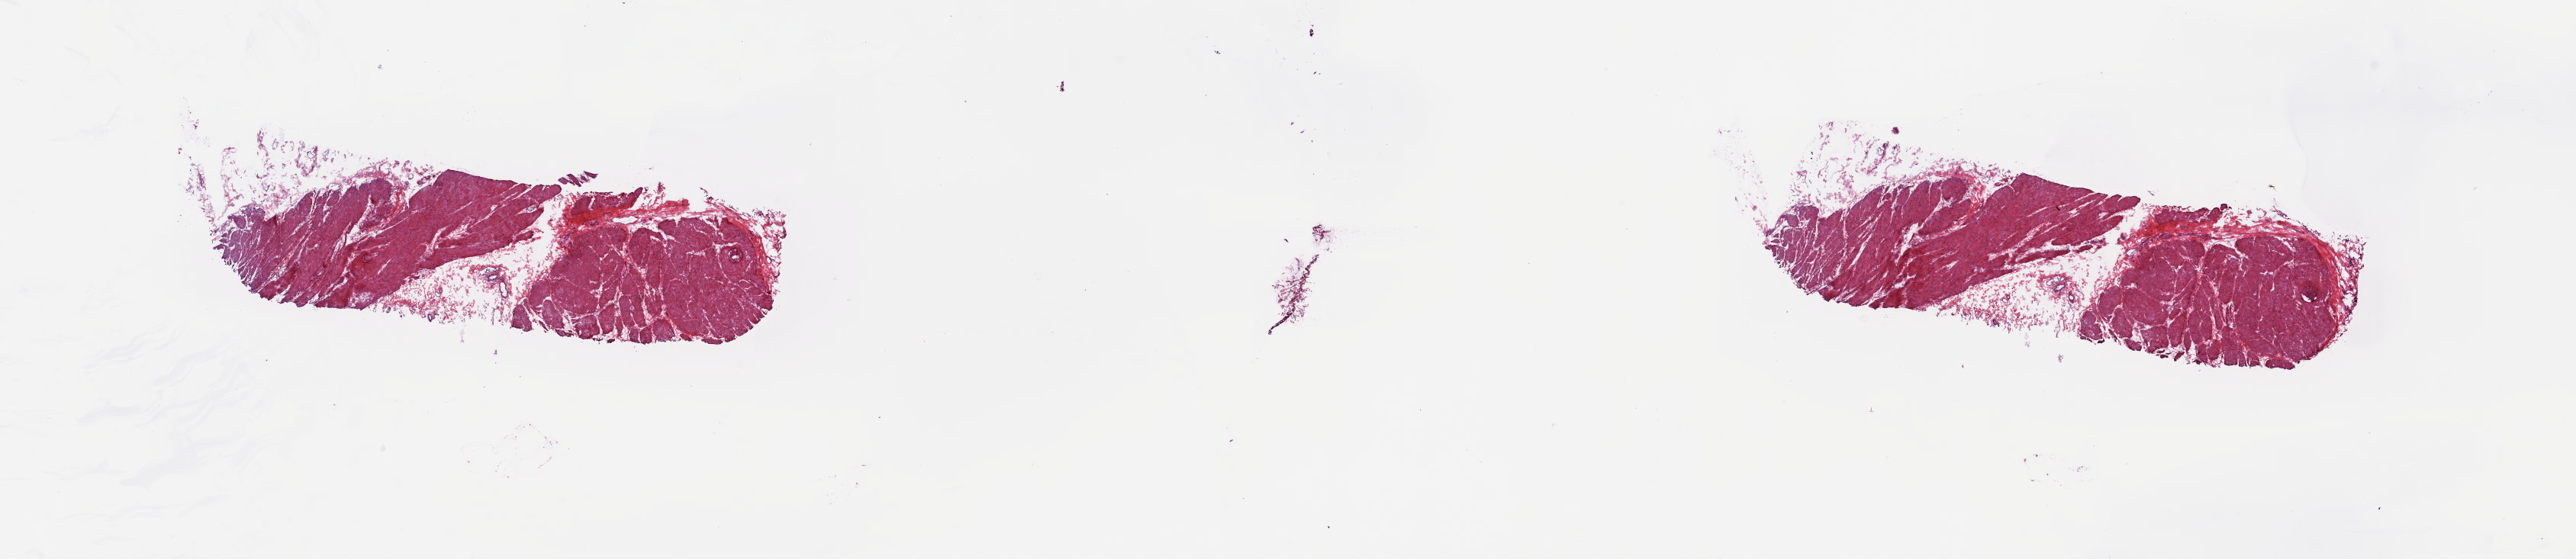
H&E whole-slide image — whole scanned area (about 26.8 x 5.8 mm, acquisition: 20x scan) shown as a low-resolution overview; frozen section; solid tissue normal (non-tumour tissue) sample from the bladder. Male patient; age at initial diagnosis 77 years. Composition of this section per pathologist review: tumour cells 0%, tumour nuclei 0%, normal cells 100%, stromal cells 0%, necrosis 0%. Inflammatory infiltration, as recorded: lymphocyte infiltration 0%, monocyte infiltration 0%, neutrophil infiltration 0%.
This section: solid tissue normal (non-tumour) sample from the same patient. Patient diagnosis: Transitional cell carcinoma.